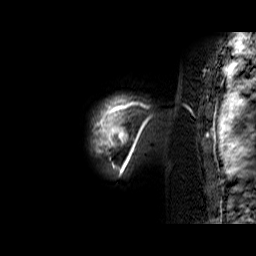
Breast MRI (dynamic contrast-enhanced), one sagittal slice; slice 56 of 60 in the series (ordered by position); dynamic contrast-enhanced series, time point 2 of 6 at this slice position (early post-contrast); 1.5 T; TE 6.4 ms, TR 32.9 ms; 4 mm slice thickness; 256 × 256 image matrix, field of view 200 × 200 mm. Female patient. Case-level facts recorded for this patient, not image findings: setting: breast cancer imaged before/during neoadjuvant chemotherapy; receptor status: triple-negative.
Structures marked on this image (semi-automatic segmentation, software-assisted and operator-edited):
- analysis volume of interest (the breast-tissue region the enhancement analysis was run in; not a lesion): bounding box (x1, y1, x2, y2) in pixels: (93, 97, 159, 174)
- tumour enhancement mask (voxels above the 100 % enhancement threshold inside the analysis volume of interest): (93, 97, 156, 174)